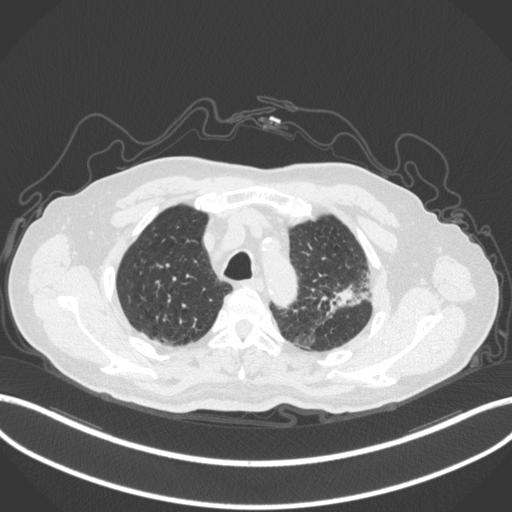
Chest CT, one axial slice; slice 242 of 331 in the series (ordered by position); lung window (W 1500 / L -600 HU); 1 mm slice thickness; 512 × 512 image matrix, field of view 400 × 400 mm. Patient: male, 79 years. Case-level facts recorded for this patient, not image findings: clinical TNM (as recorded): T2a N1 M1.
Structures marked on this image (bounding box drawn by a radiologist):
- lung tumour (recorded histology: adenocarcinoma): bounding box <326,273,372,318> (left, top, right, bottom; pixels)